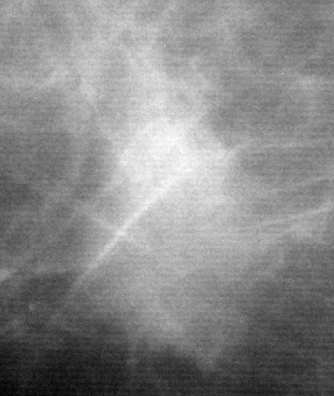
Region of interest cut from a scanned film mammogram (one marked finding), right breast, MLO view.
- Finding: mass, shape oval, margins microlobulated; BI-RADS assessment category 5; pathology (as recorded): malignant.